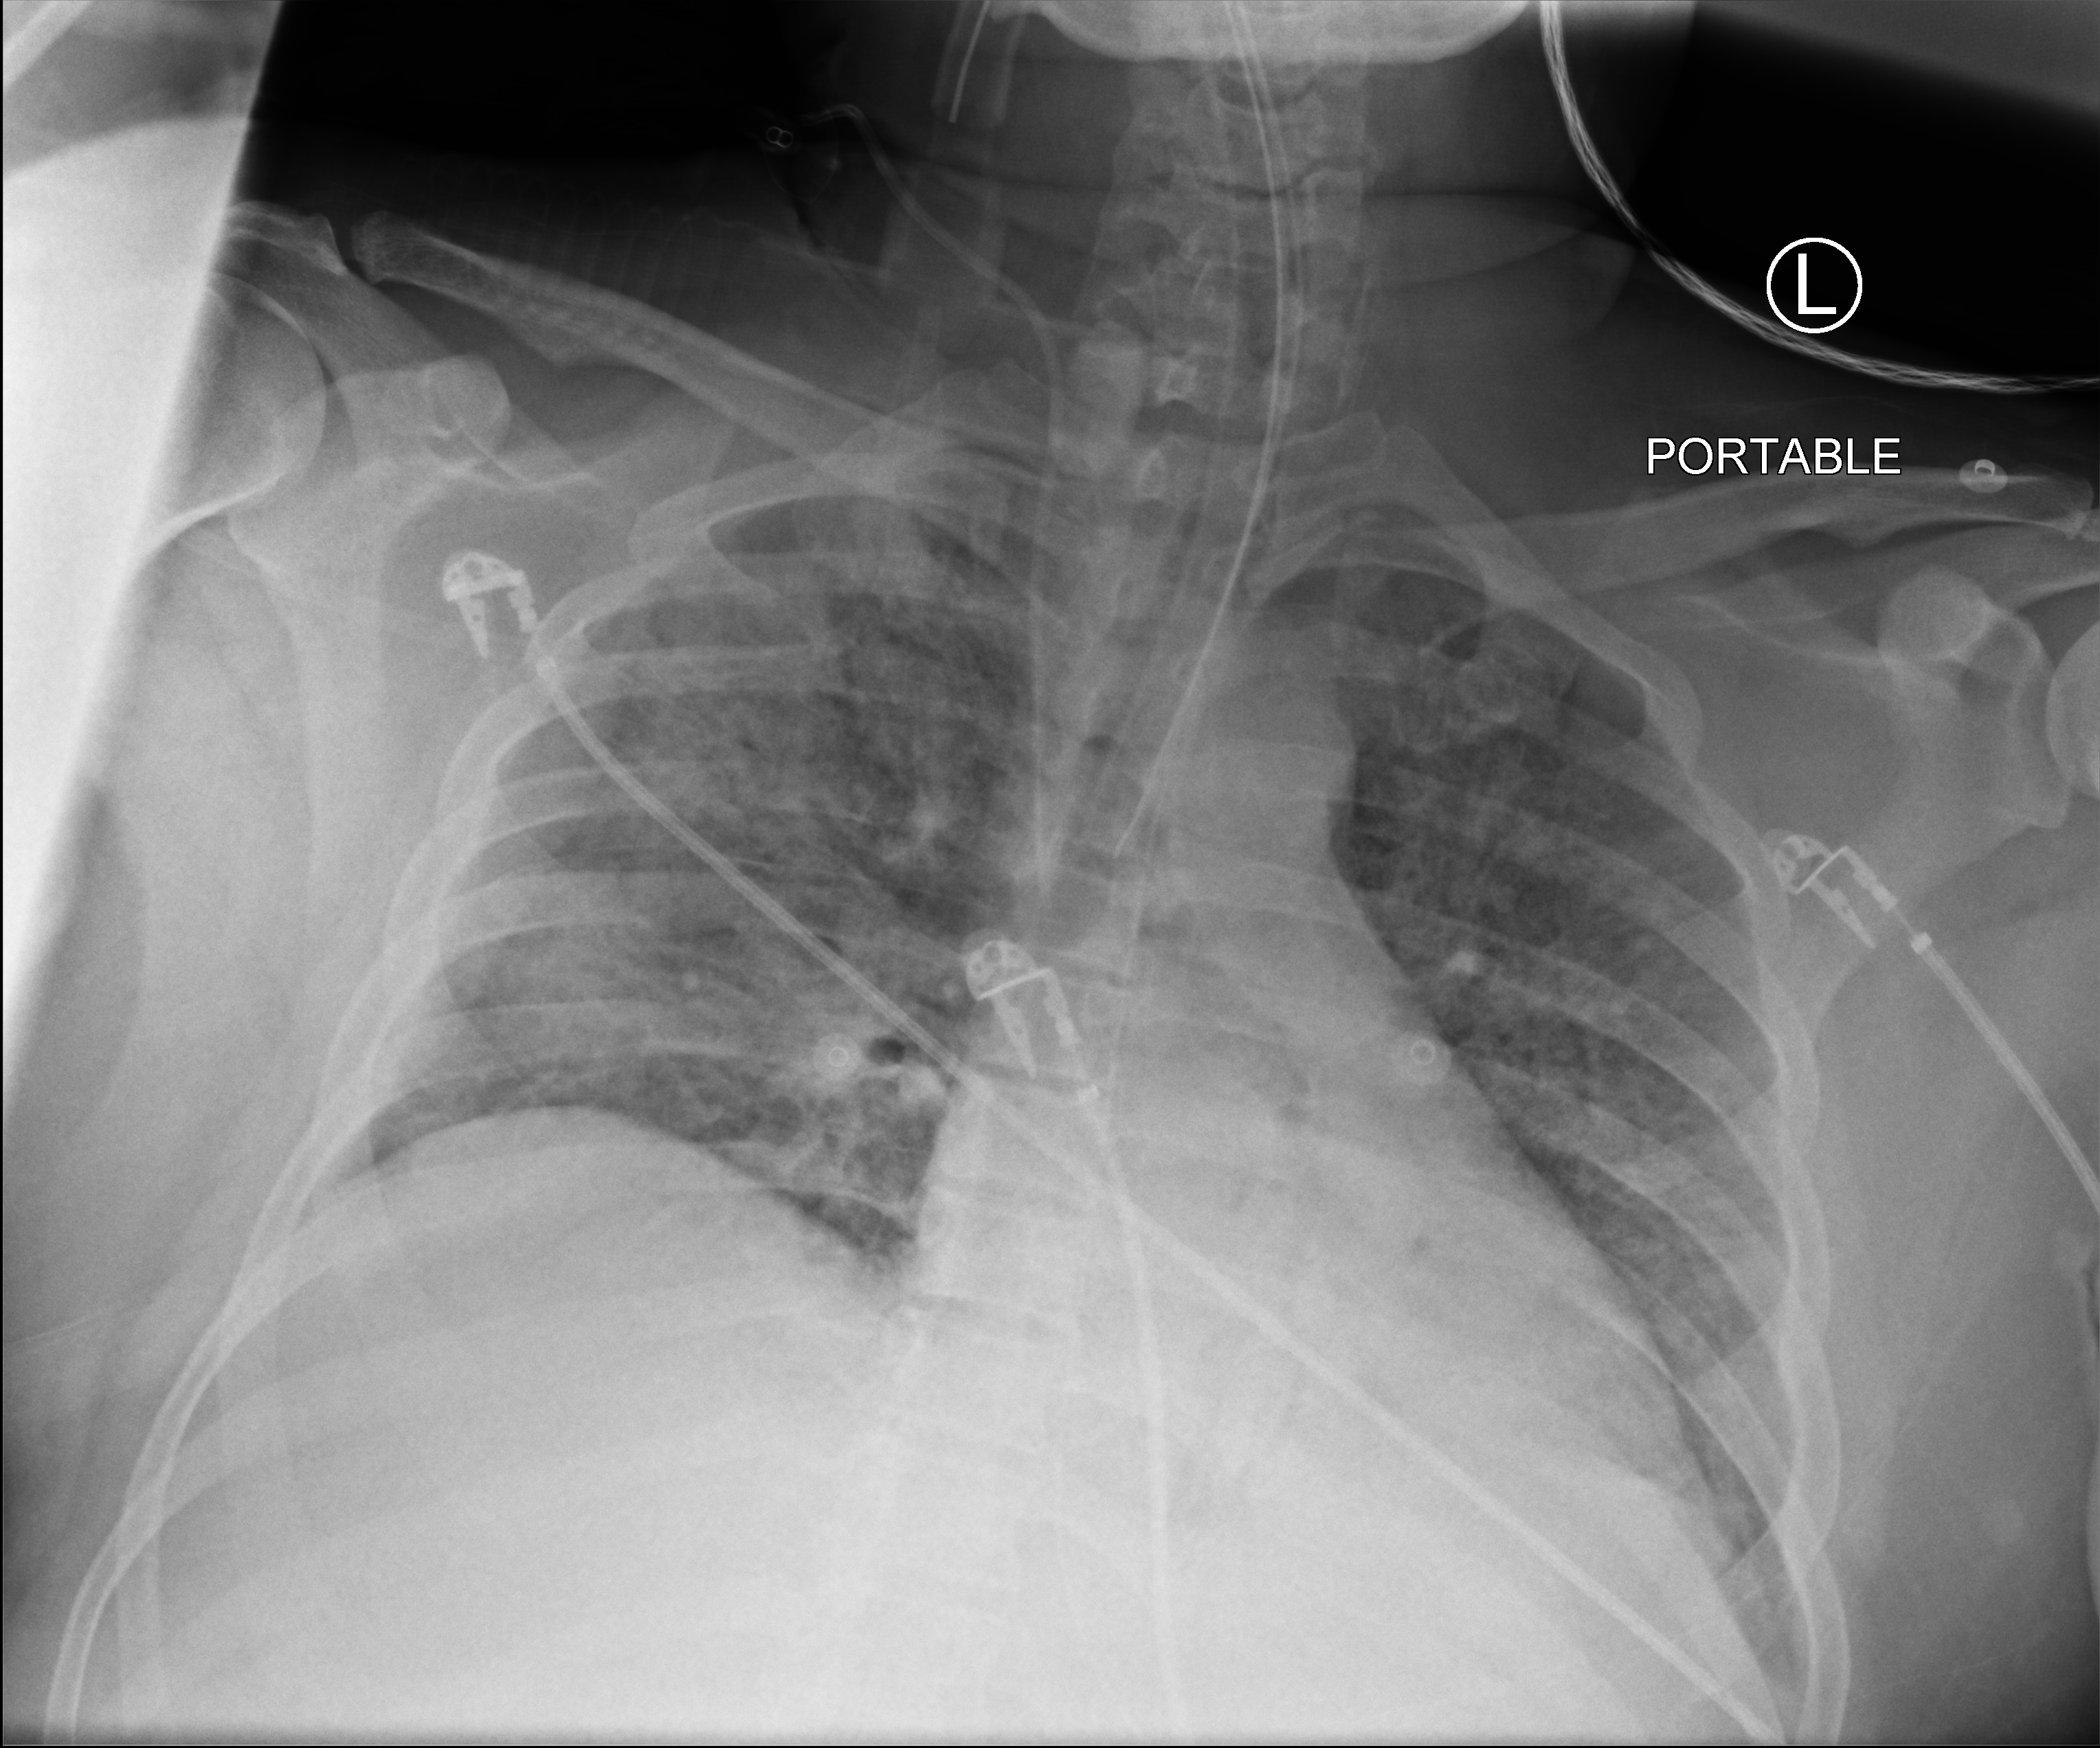
Bedside chest radiograph (computed radiography); anteroposterior (AP) projection. Patient hospitalised with COVID-19; male, aged 18–59 years.
Hospital-stay facts (about this admission, not read from this image; timing relative to this image not recorded):
- mechanically ventilated during this hospital stay: yes